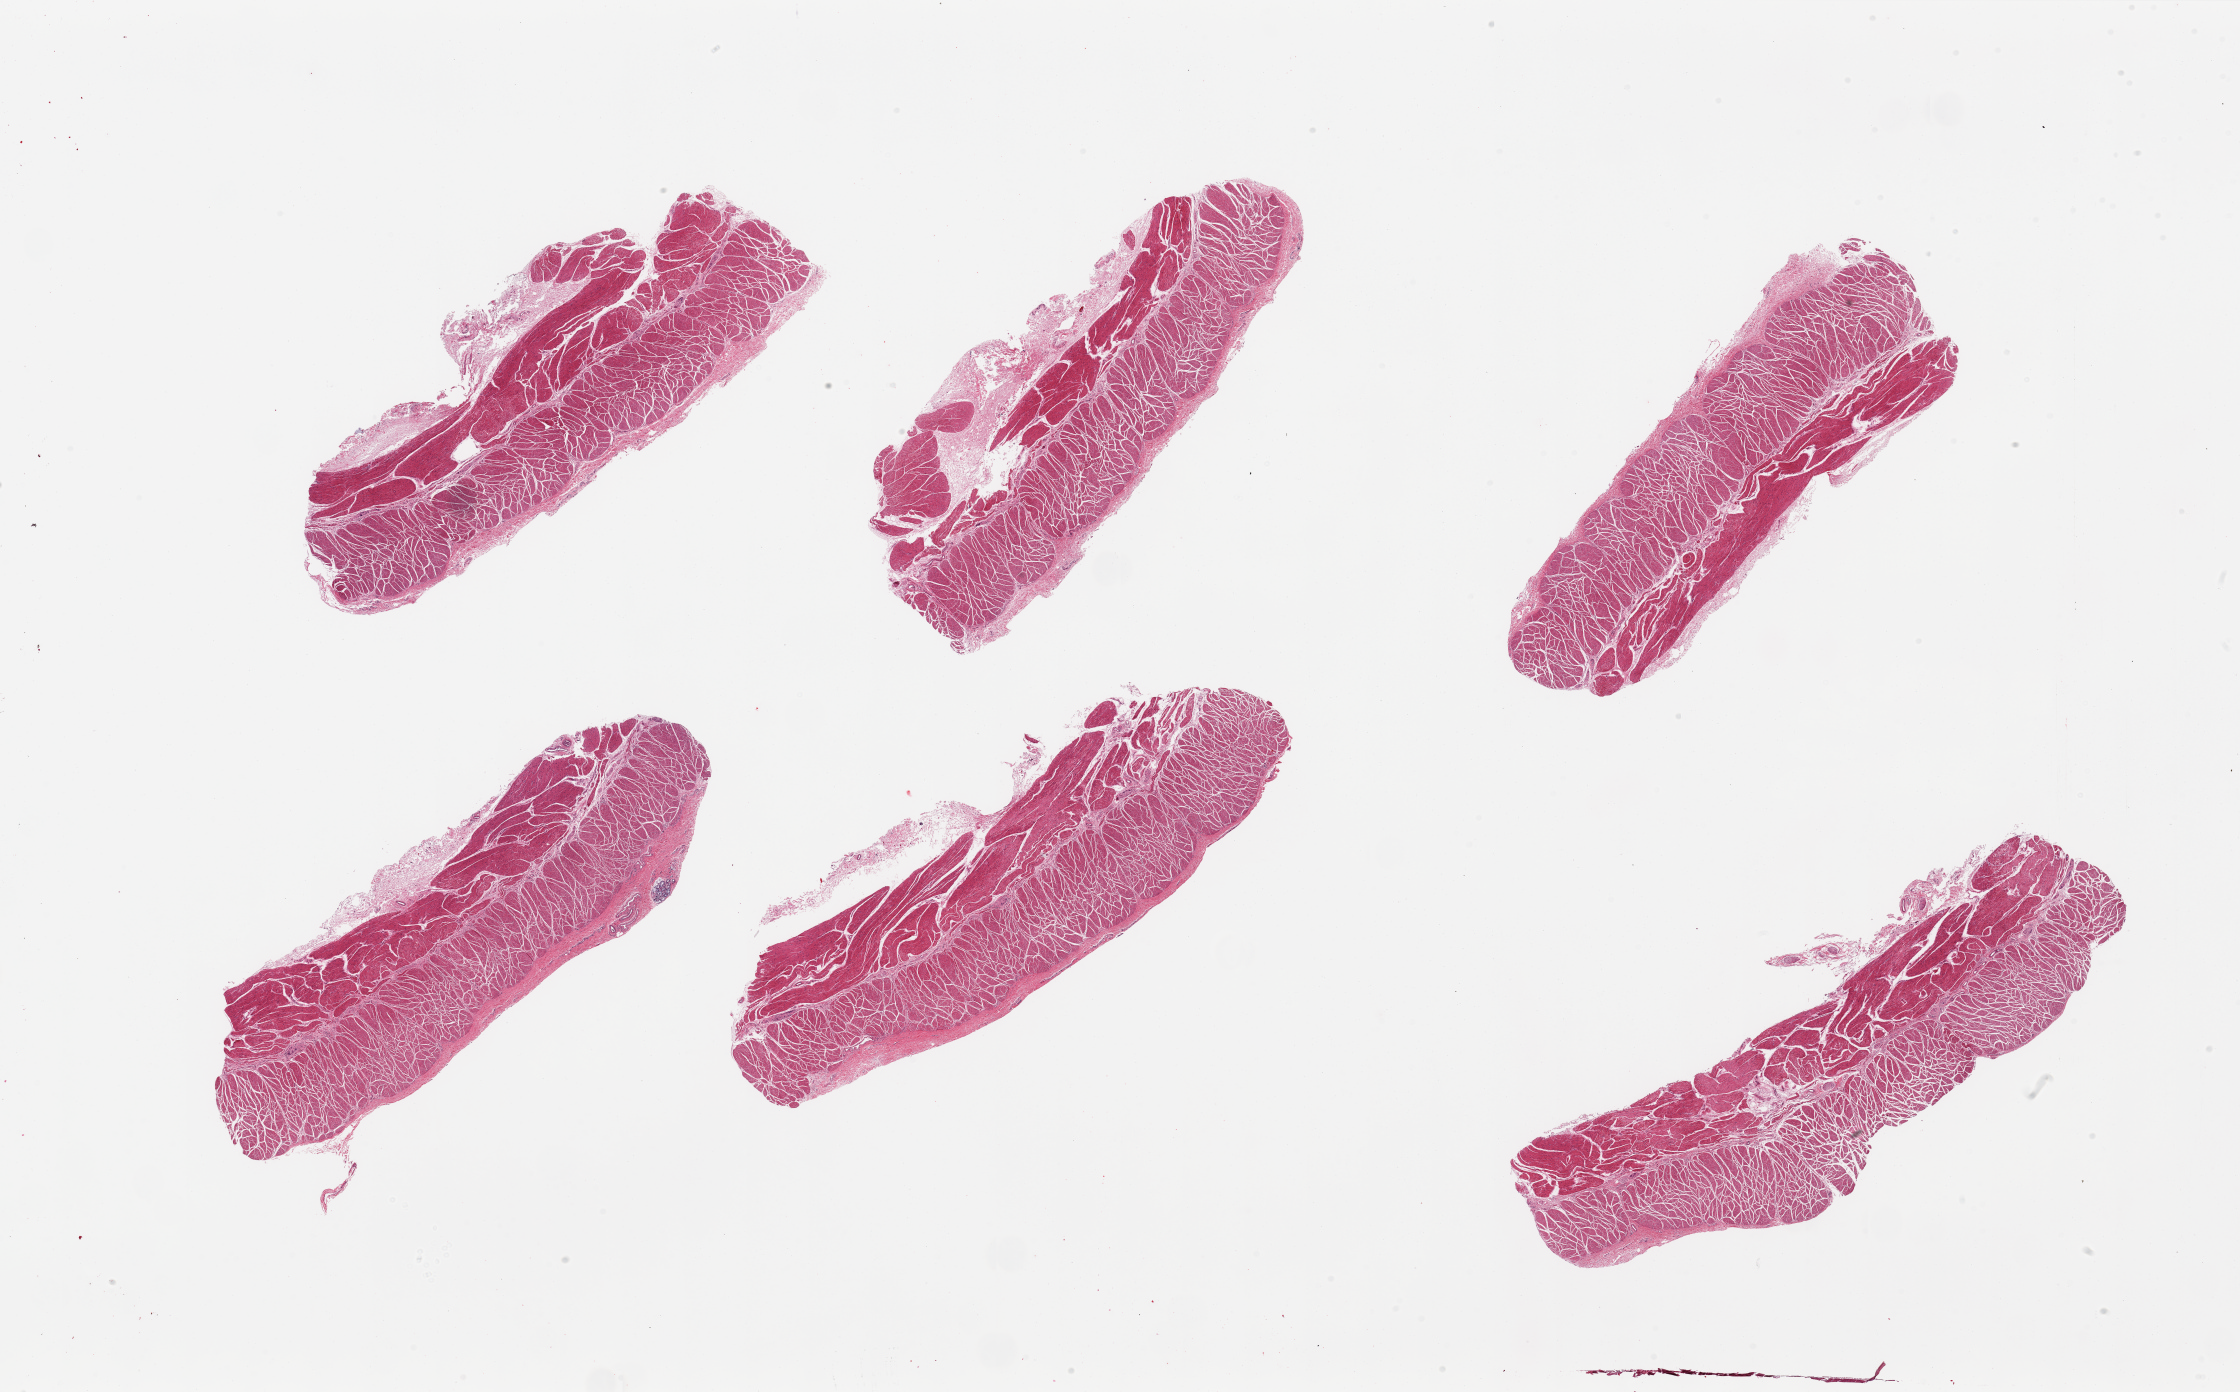
H&E whole-slide image, a low-resolution overview of the entire scanned area, about 35.4 x 22.0 mm (from a 20x scan), PAXgene-fixed paraffin-embedded (PFPE) section, sampled site (target tissue): esophageal muscle, tissue donor sample.
Review note (as recorded): 6 pieces; well dissected muscularis.